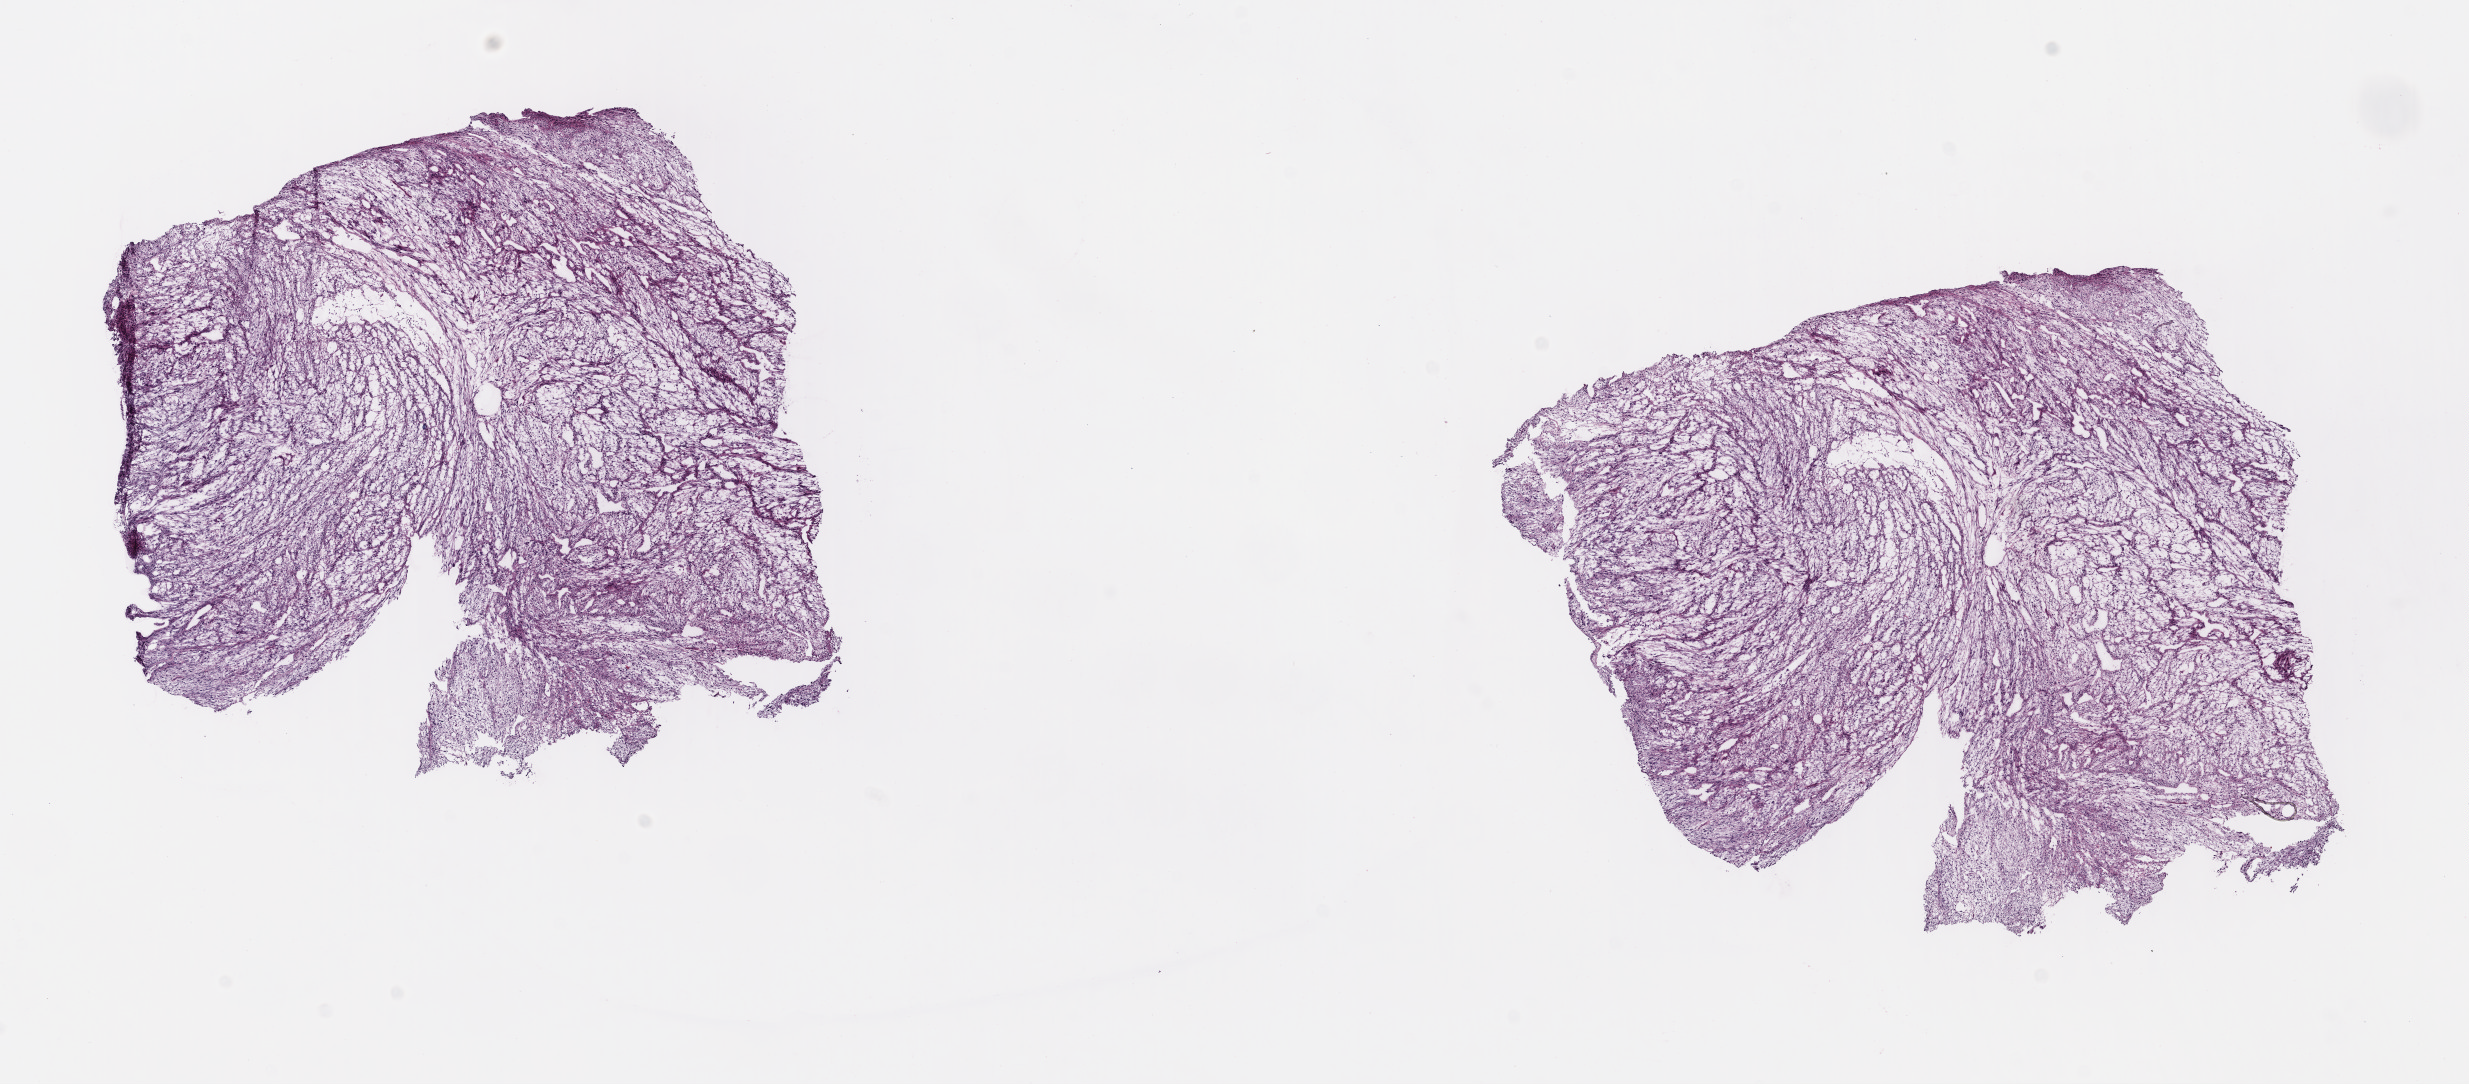
Digitized H&E-stained tissue section (whole slide), a low-resolution overview of the entire scanned area, about 19.4 x 8.5 mm, frozen section, retroperitoneum and peritoneum, primary tumour sample. Patient: female, age at initial diagnosis 65 years. Pathologist review of this section (percent, as recorded): tumour cells 80%, tumour nuclei 100%, normal cells 0%, stromal cells 20%, necrosis 0%. Infiltration values recorded for this section: lymphocyte infiltration 0%, monocyte infiltration 0%, neutrophil infiltration 0%.
Diagnosis: Leiomyosarcoma, NOS (retroperitoneum).